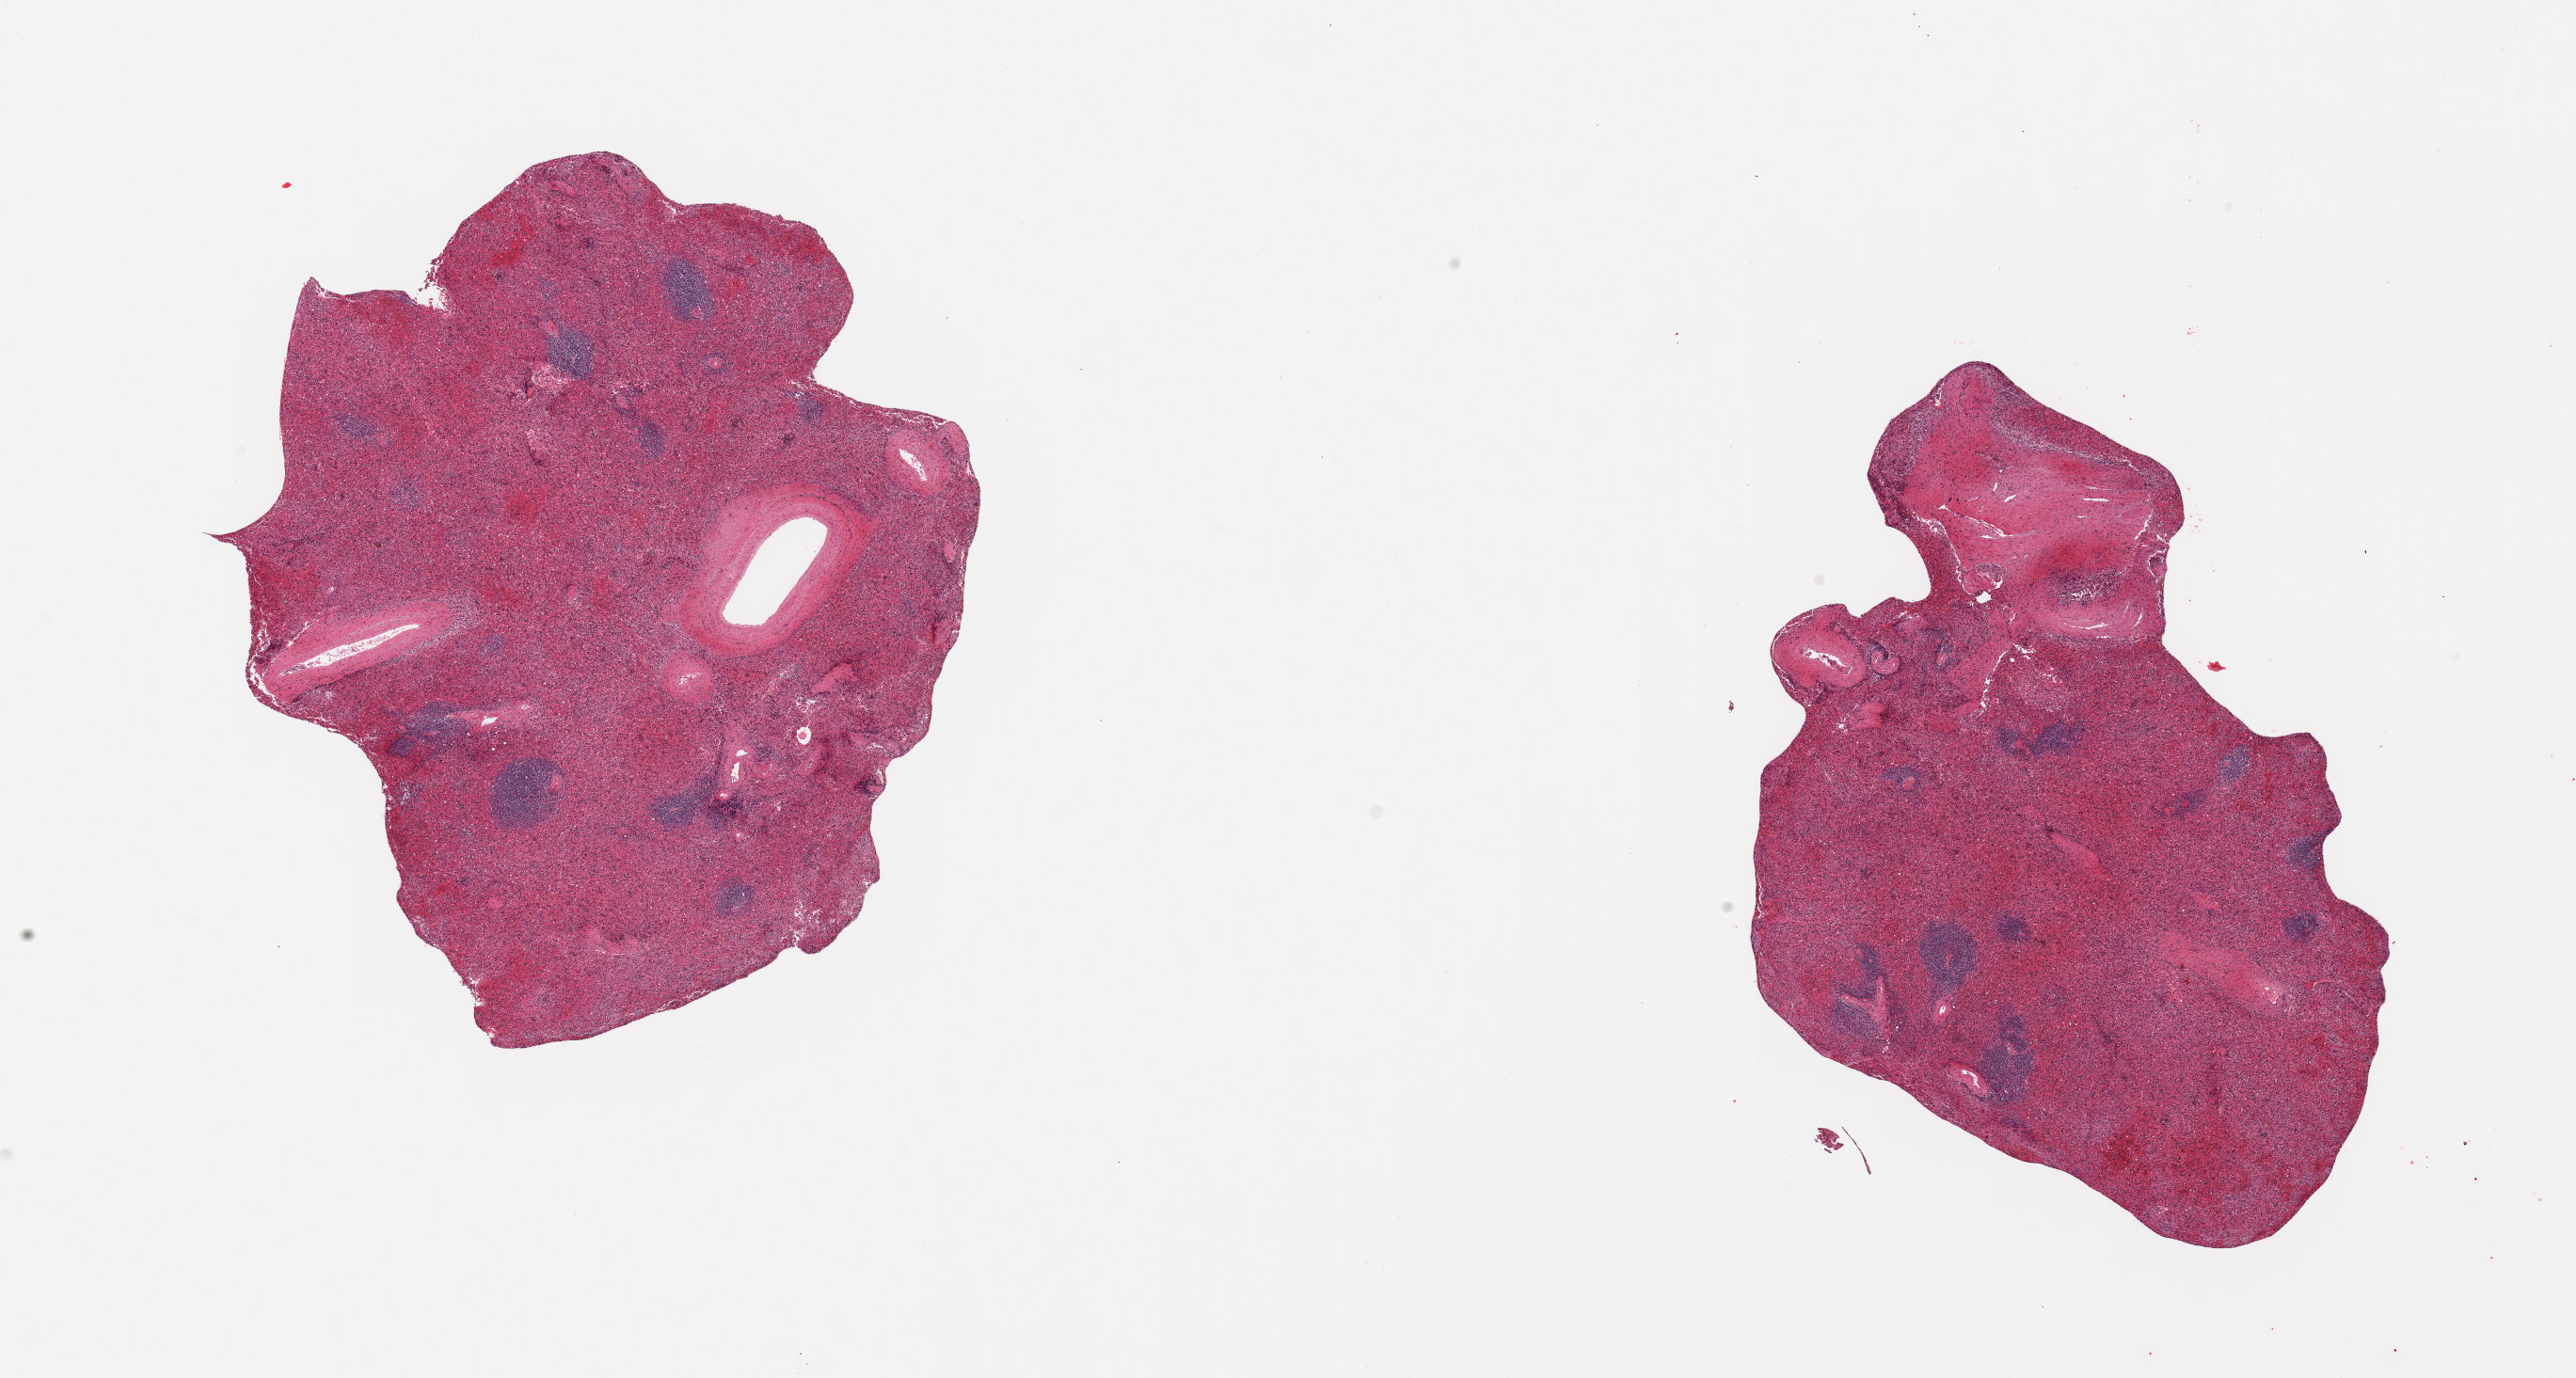
H&E whole-slide image, brightfield — whole scanned area (about 21.7 x 11.6 mm, acquisition: 20x scan) shown as a low-resolution overview; PAXgene-fixed paraffin-embedded (PFPE) section; section of spleen (target tissue); tissue donor sample. Male donor.
- pathologist's review note for this sample: 2 pieces; patchy vascular congestion